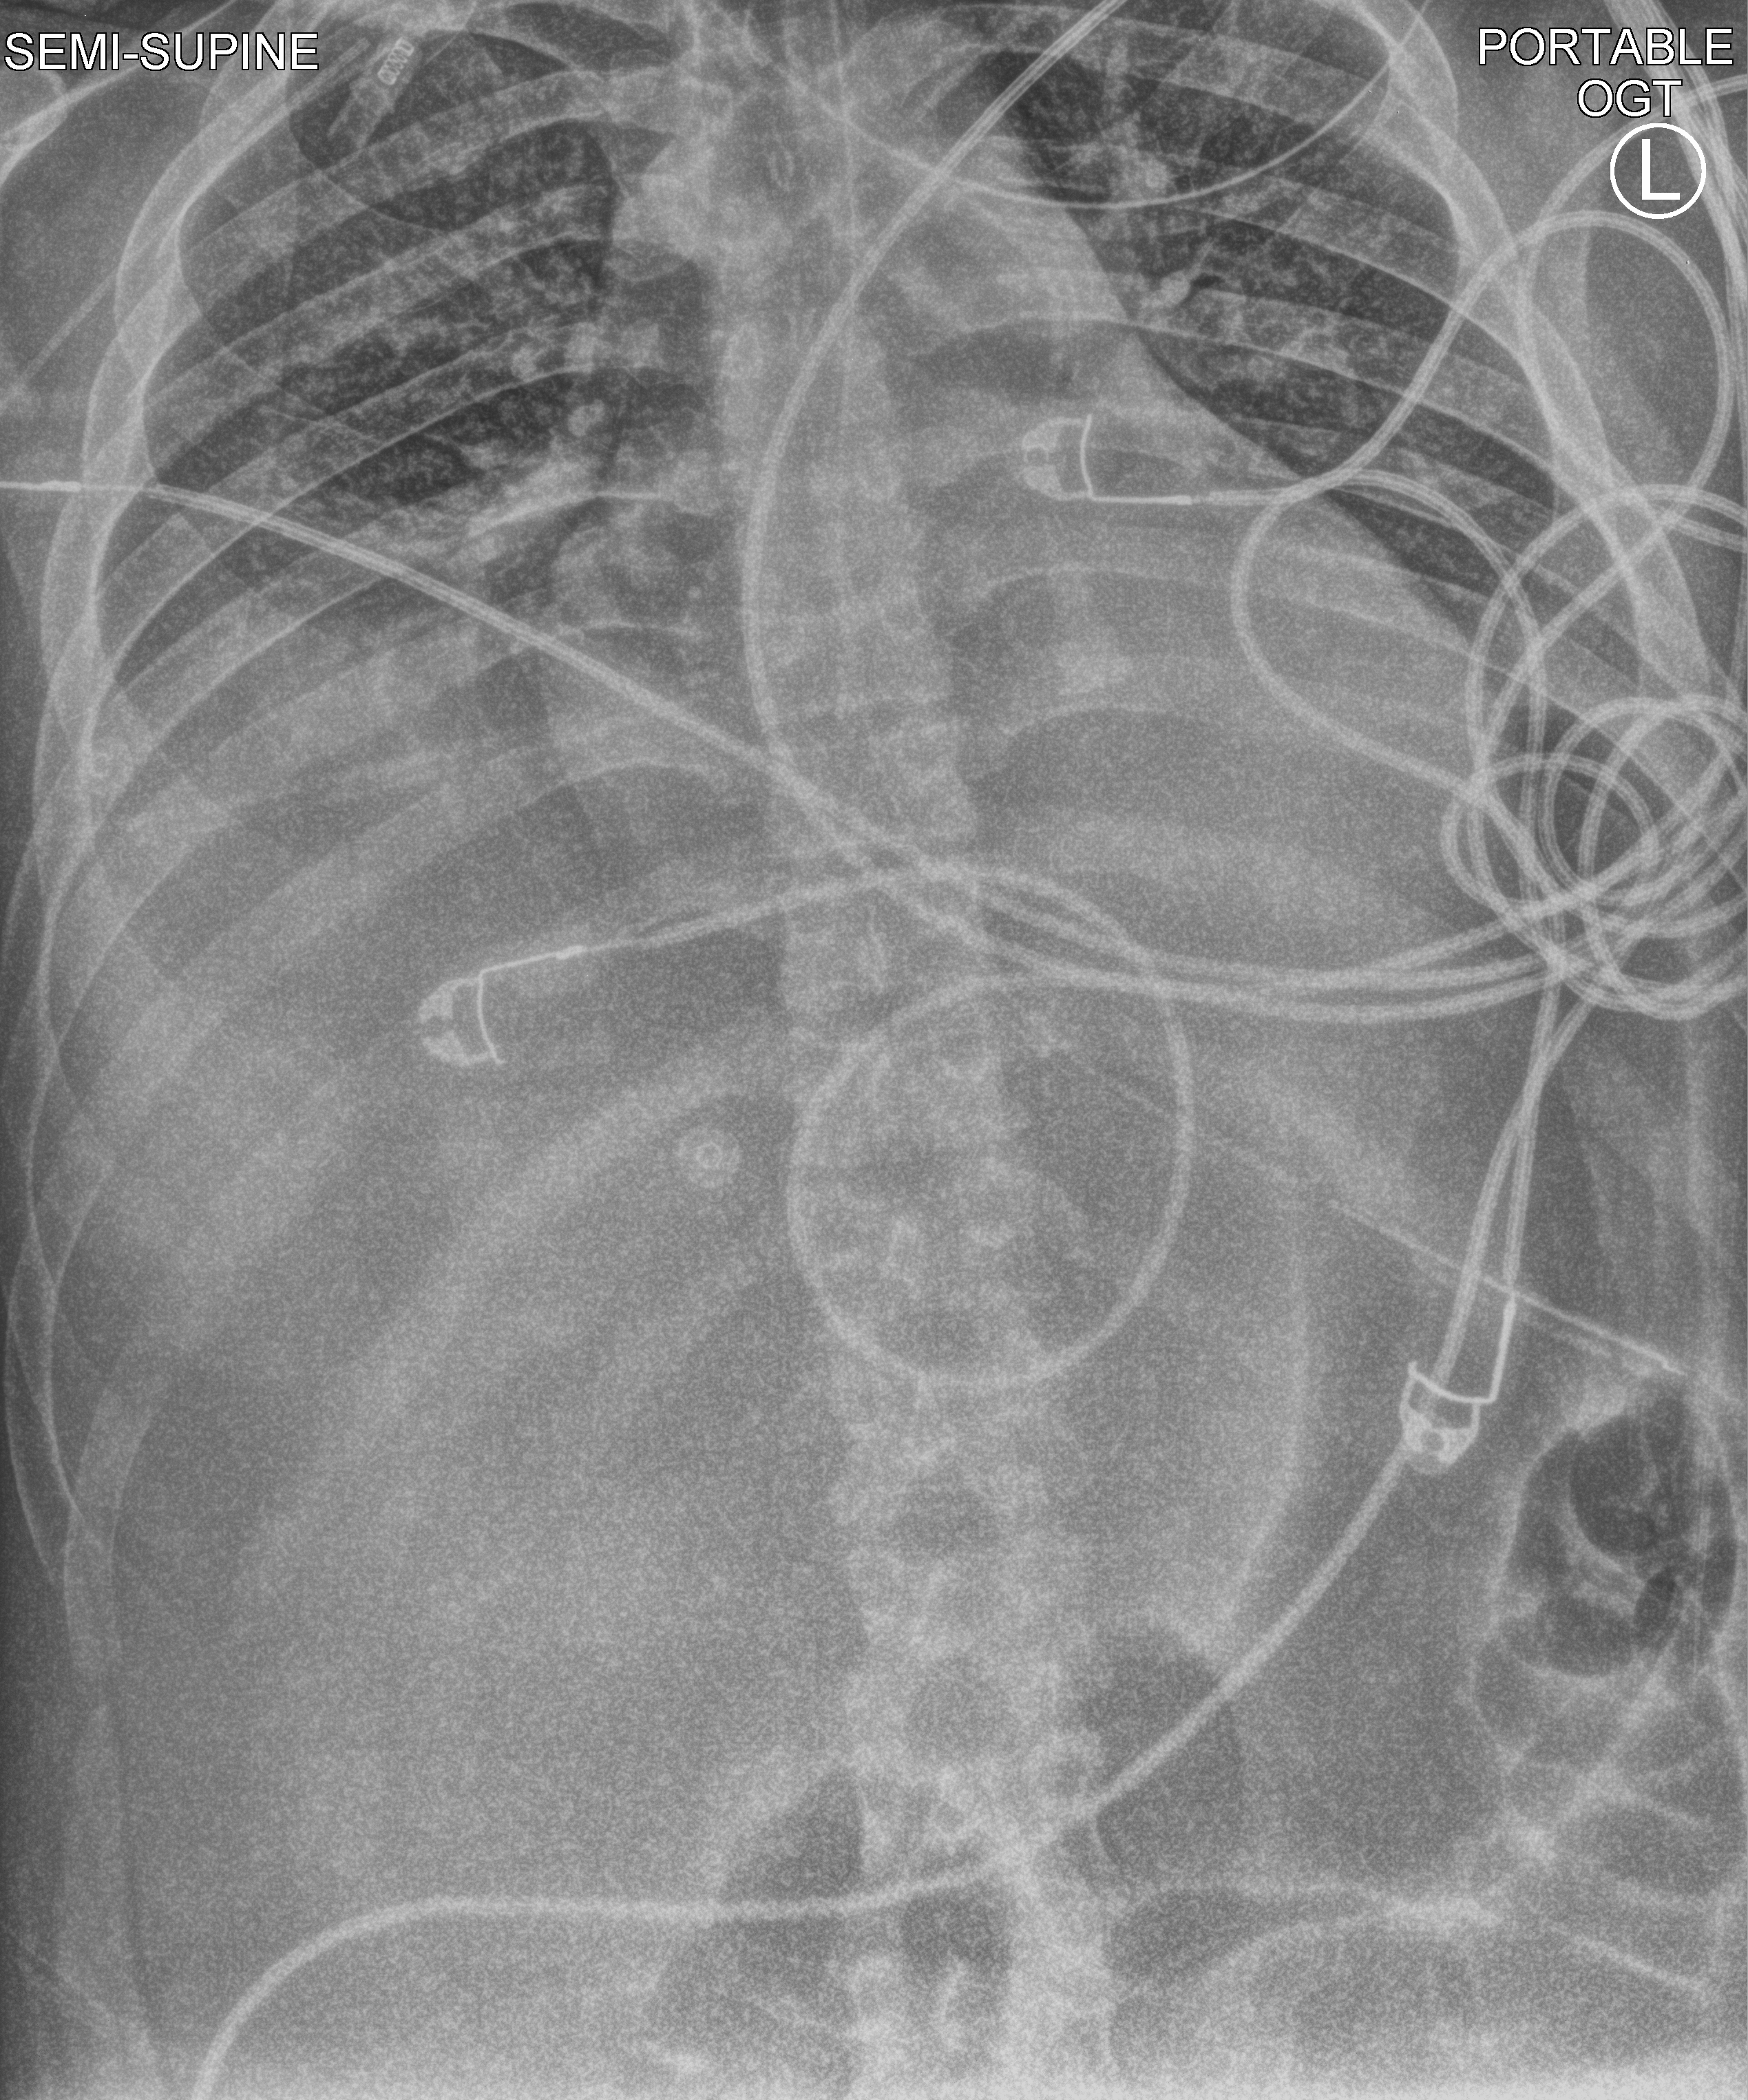
Portable chest radiograph, anteroposterior (AP) projection. Male patient hospitalised with COVID-19, age 18–59 years.
From the hospital-stay record, not from the radiograph (when in the stay this image was taken is not recorded): mechanically ventilated during this hospital stay: yes.